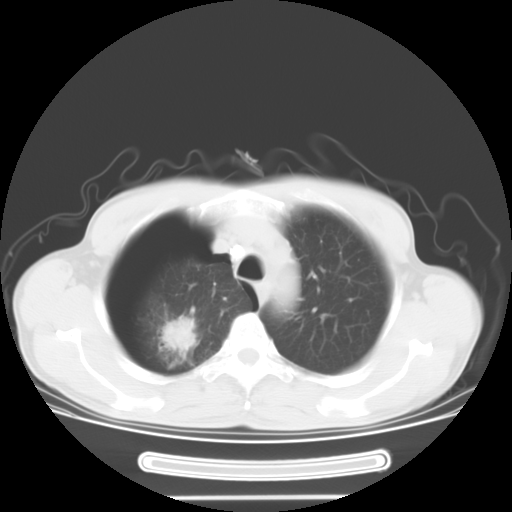
Chest CT, one axial slice. Slice 27 of 34 in the series (ordered by position). 120 kVp. Lung window (W 1500 / L -600 HU). 10 mm slice thickness. 512 × 512 image matrix, field of view 375 × 375 mm. Male patient. From the clinical record (not read from this slice): clinical TNM (as recorded): T1c N0 M0.
Annotated regions visible in this slice (bounding box drawn by a radiologist):
- lung tumour (recorded histology: adenocarcinoma): bounding box (x1, y1, x2, y2) in pixels: (163, 312, 202, 348)